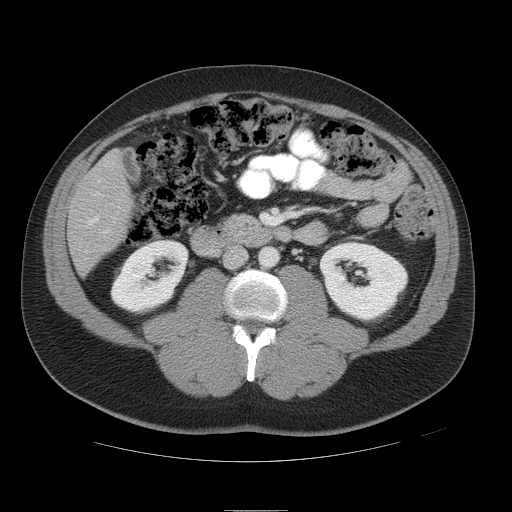
Contrast-enhanced abdominal CT, one axial slice; position 16 of 49 along the scan axis; reconstruction kernel STANDARD; 120 kVp; intravenous contrast given; soft-tissue window (W 400 / L 40 HU); 512 × 512 image matrix. Male patient, age 52 years. From the clinical record (not read from this slice): diagnosis: colorectal cancer liver metastases, imaged before liver resection; multiple liver metastases: yes; largest metastasis: 5.1 cm.
Annotated regions visible in this slice (expert manual segmentation):
- hepatic veins: box from (x=88, y=217) to (x=99, y=225) px
- liver: (x=69, y=154)–(x=131, y=273)
- portal vein (with intrahepatic branches): (x=93, y=162)–(x=109, y=233)